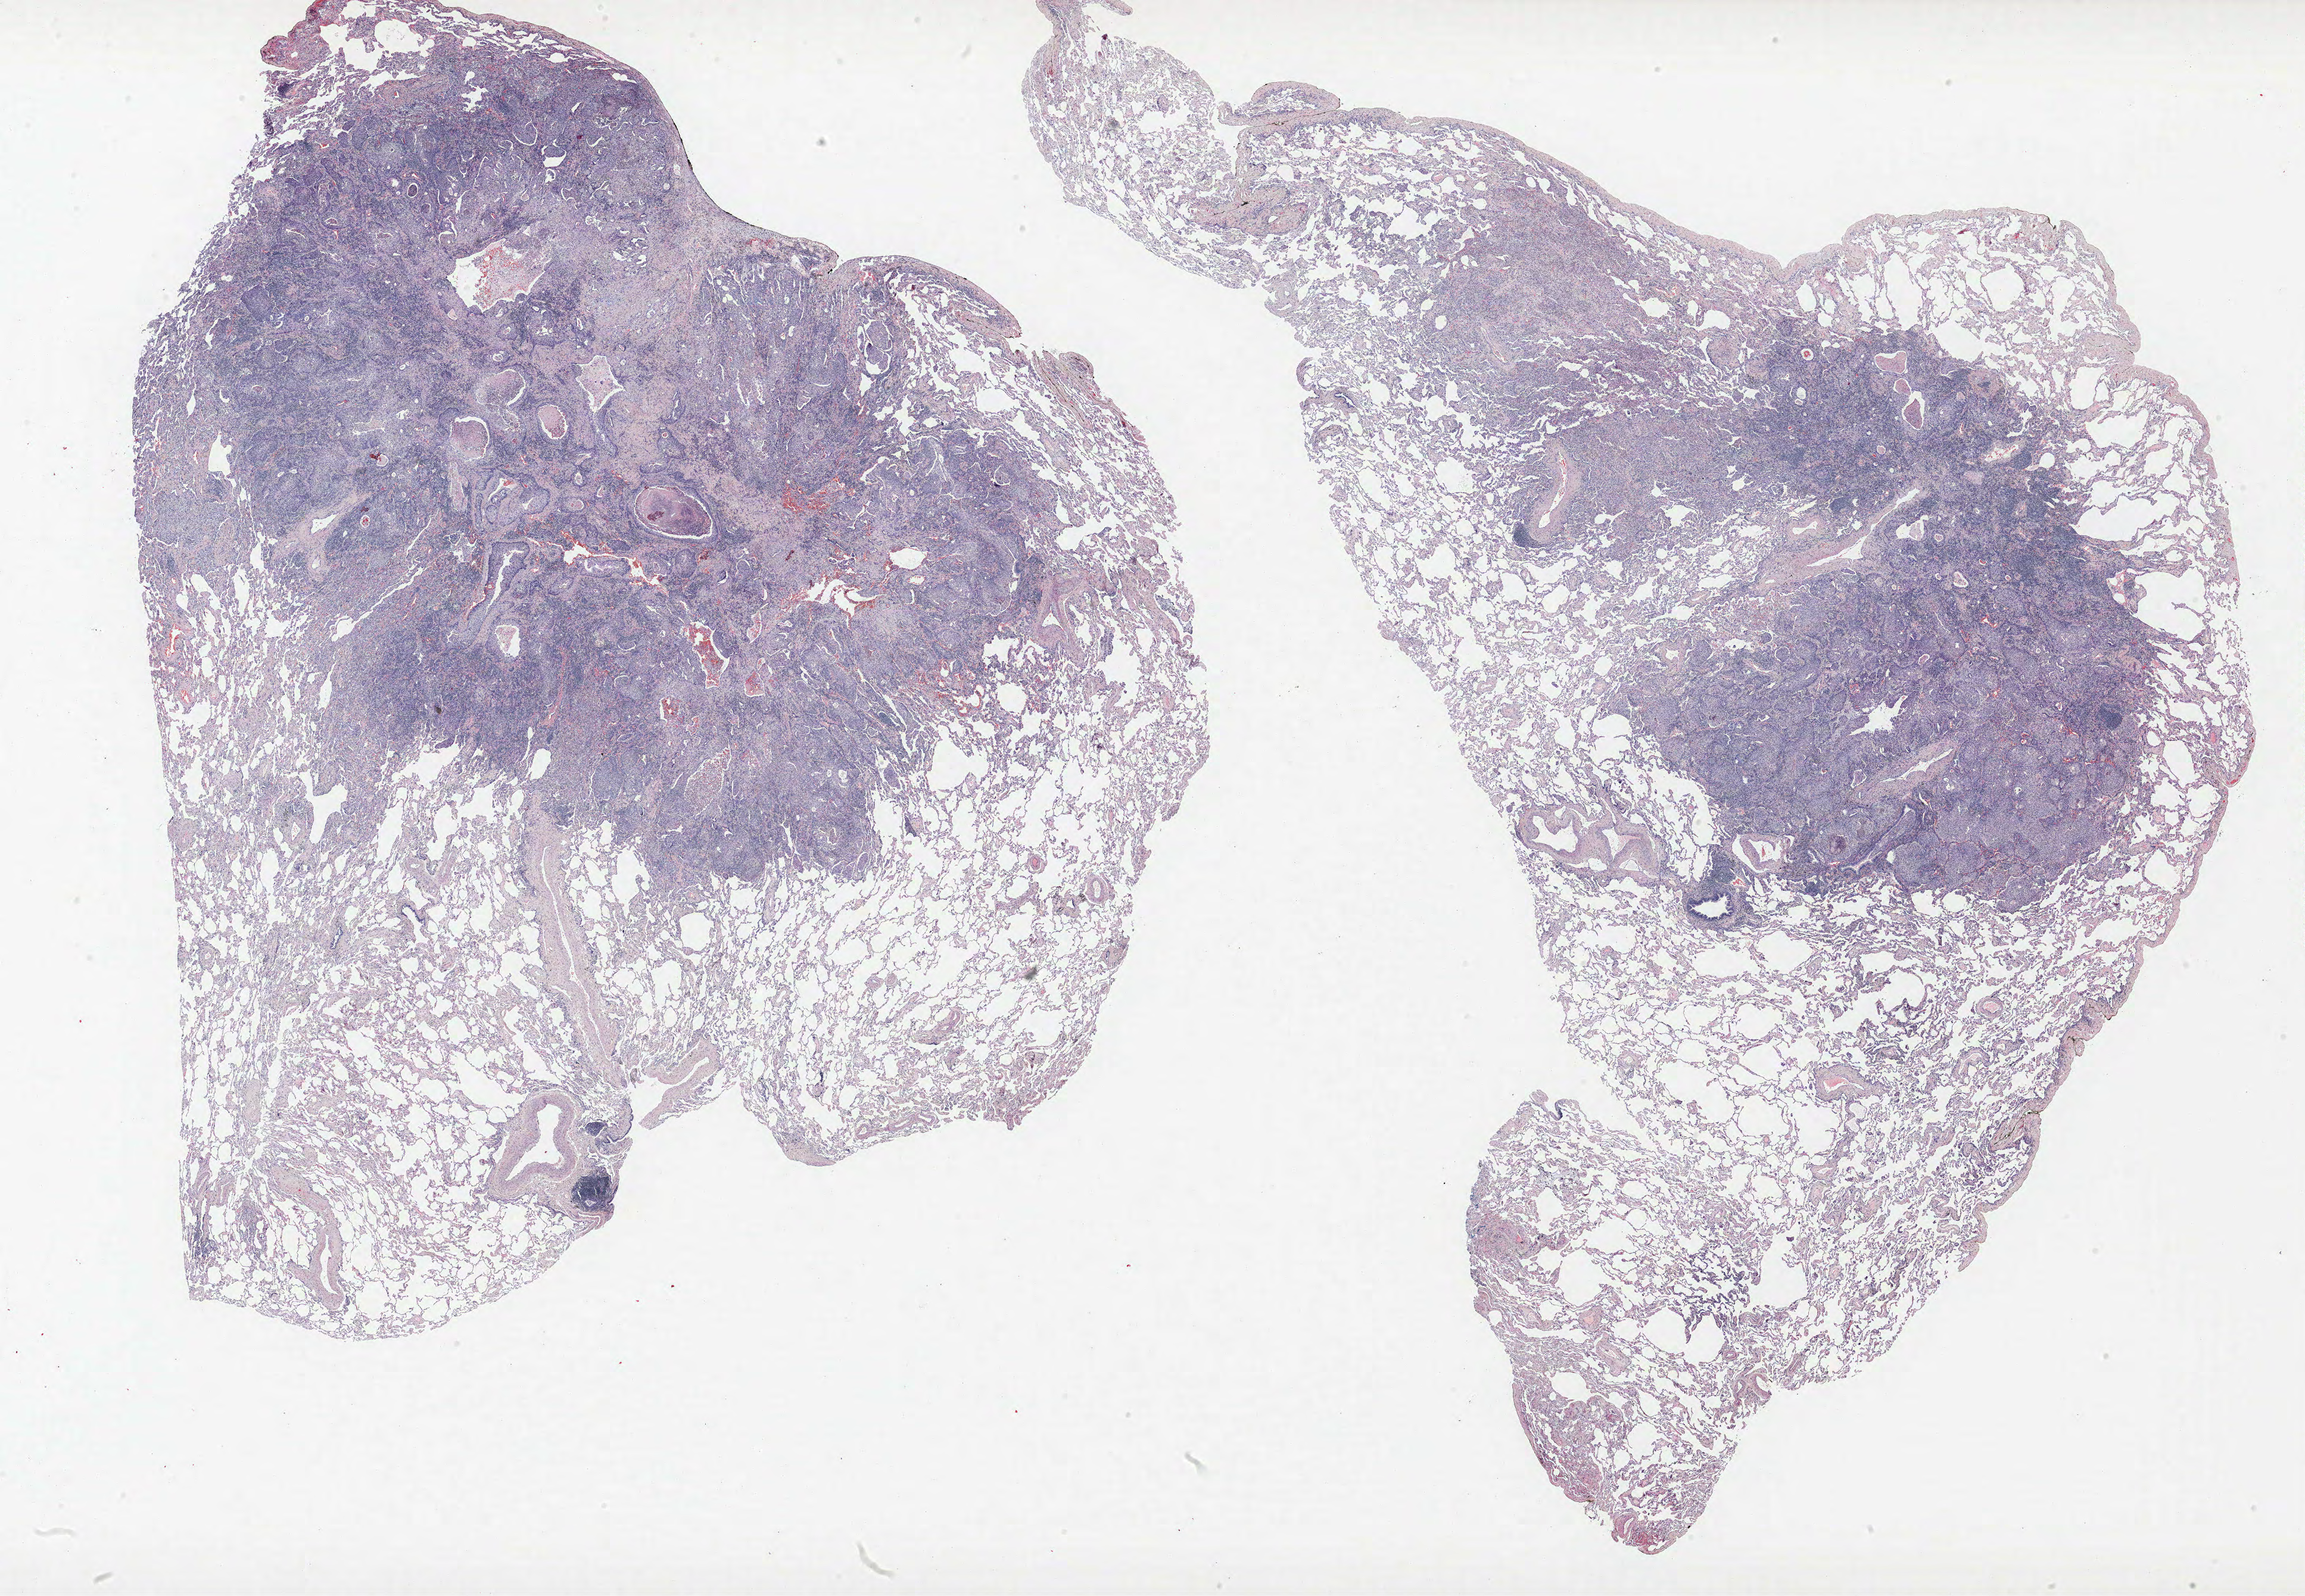
Whole-slide histology image, H&E — whole scanned area (about 31.0 x 21.4 mm, acquisition: 40x scan) shown as a low-resolution overview, FFPE section, lung. Male patient, aged 67 at enrolment. Former smoker at enrolment. Grade: moderately differentiated (G2).
Participant's lung-cancer diagnosis: Squamous cell carcinoma, large cell, nonkeratinizing, NOS (ICD-O-3 8072/3). Tumour size (pathology): 15 mm. Stage (AJCC 6th edition): IA. Primary tumour location (clinical record): left upper lobe.